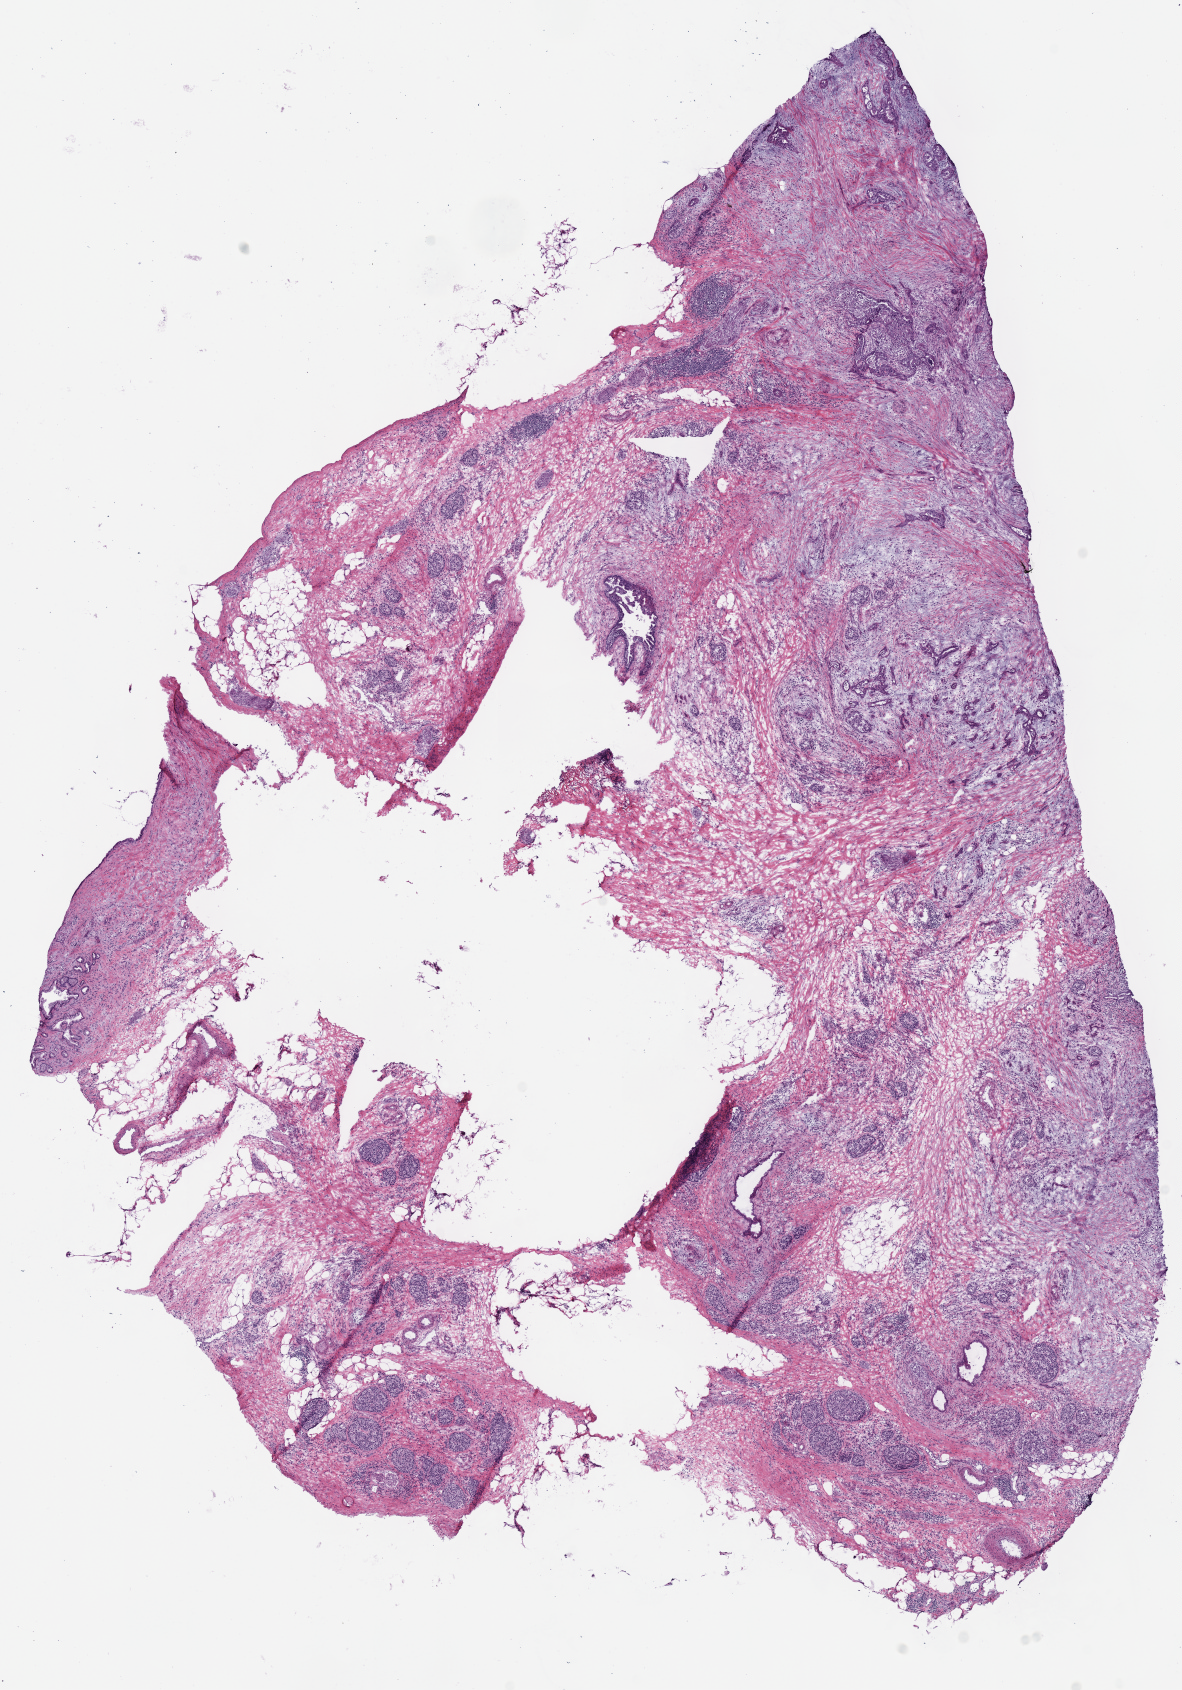
Hematoxylin and eosin (H&E) stained whole-slide image, whole scanned area (about 9.3 x 13.3 mm, from a 40x scan) shown as a low-resolution overview, frozen section, sample: primary tumour, pancreas. Female, age 53 years at initial diagnosis. Histologic grade: G2 (moderately differentiated). Slide review estimates, as recorded: tumour cells 75%, tumour nuclei 60%, normal cells 0%, stromal cells 25%, necrosis 0%.
TNM: T3 N1 M0. AJCC pathologic stage: IIB (6th edition). Pathologic diagnosis: Infiltrating duct carcinoma, NOS. Lymph nodes positive (case pathology): 2 of 17 examined.